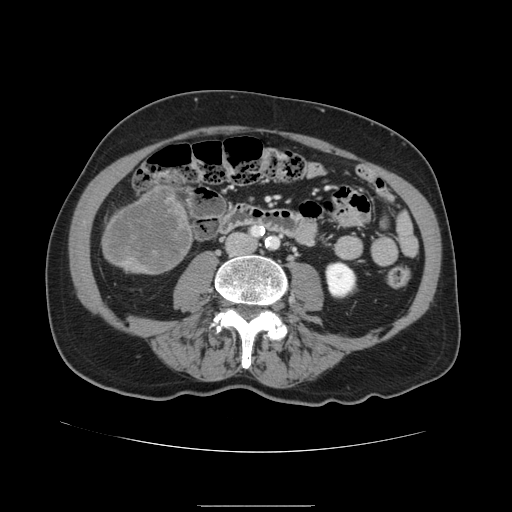
Contrast-enhanced abdominal CT, one axial slice. Slice 22 of 168 in the series (ordered by position). Intravenous contrast given. Soft-tissue window (W 400 / L 40 HU). 512 × 512 image matrix, field of view 386 × 386 mm. Male patient, age 74 years. From the clinical record (not read from this slice): diagnosis: colorectal cancer liver metastases, imaged before liver resection; multiple liver metastases: no; largest metastasis: 14.5 cm; chemotherapy before resection: no.
Structures marked on this image (expert manual segmentation):
- liver: bounding box [x1, y1, x2, y2] px = [103, 183, 193, 275]
- liver metastasis: [107, 187, 190, 271]